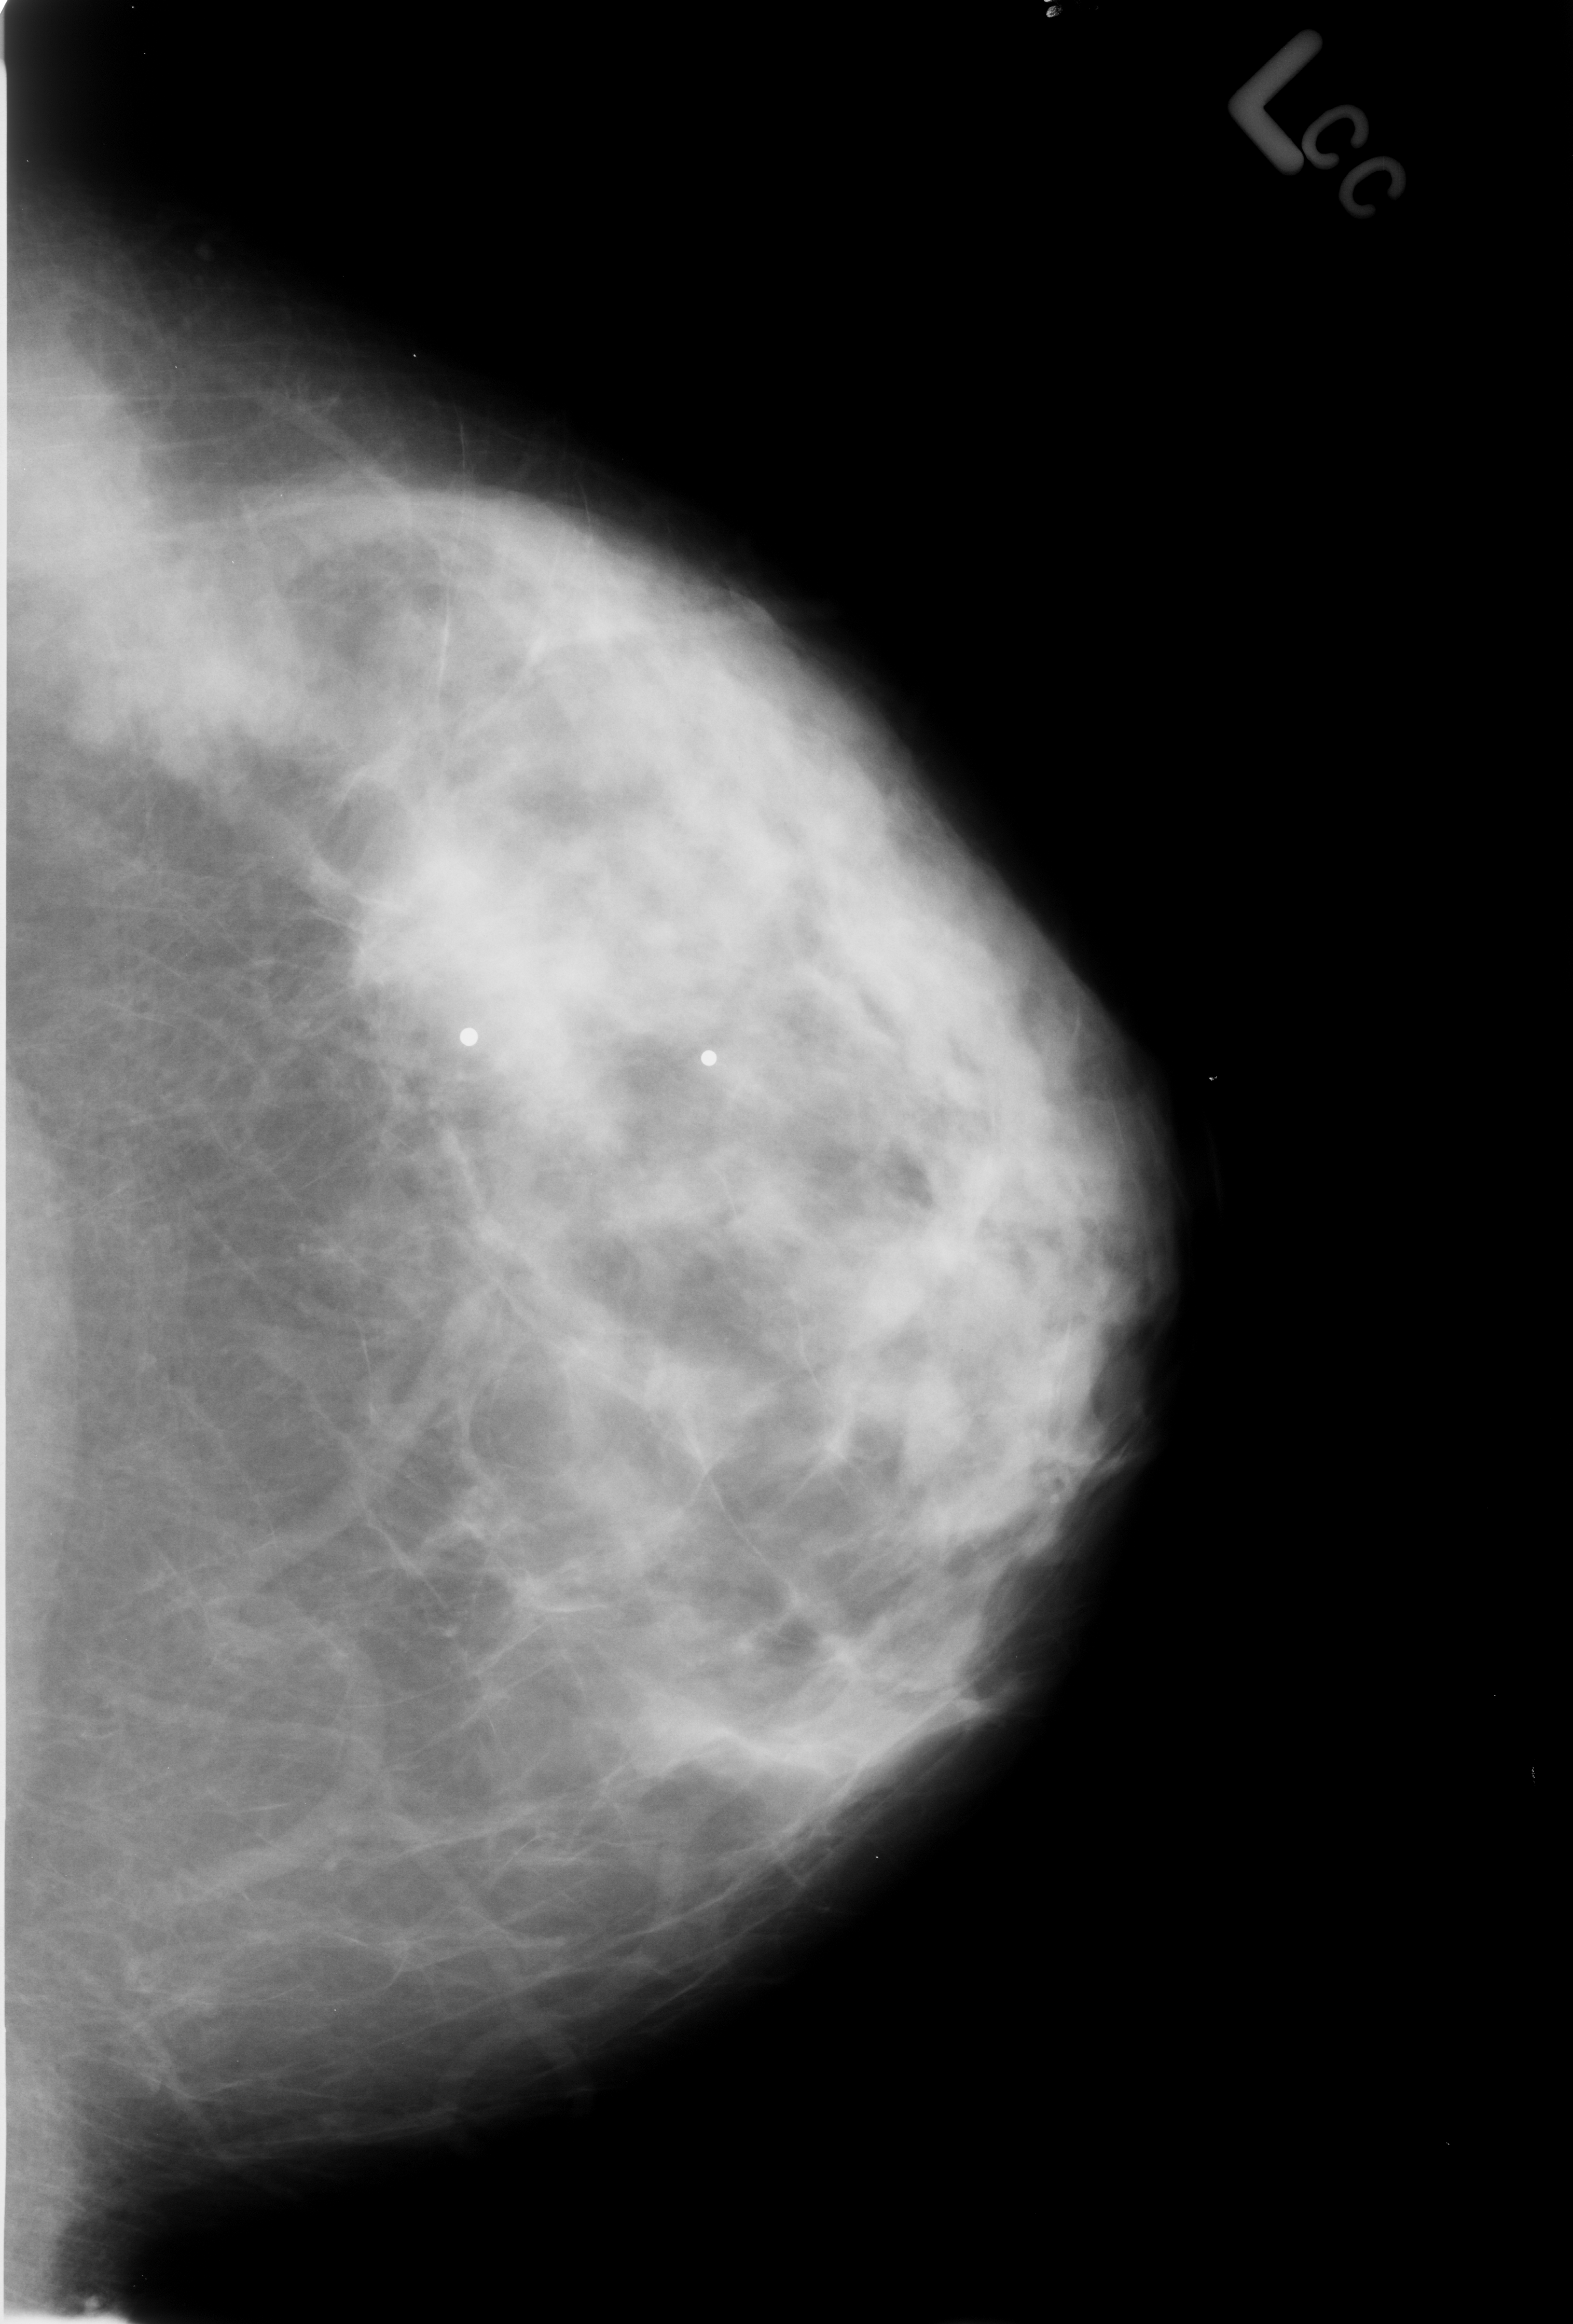
Digitized screen-film mammogram; left breast; craniocaudal (CC) view; BI-RADS breast density category 3 (scale 1–4); 1573 × 2324 image matrix.
Expert-marked regions of interest on this image (one box per marked abnormality):
- mass, shape focal asymmetric density; BI-RADS assessment category 2; subtlety rating 4 on a 1 (subtle) to 5 (obvious) scale; outcome (as recorded, no biopsy): benign without callback (not worked up further): bounding box <28,415,266,782> (left, top, right, bottom; pixels)